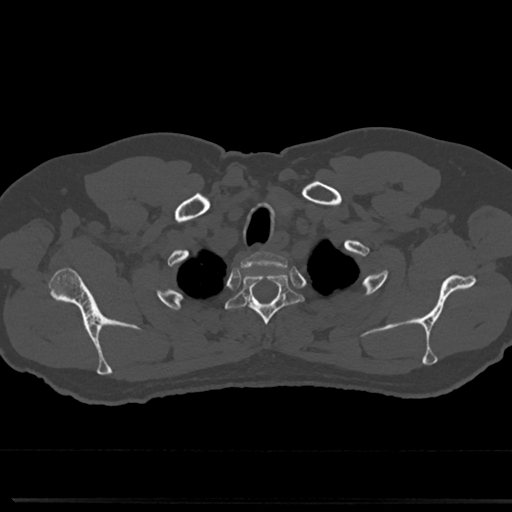
CT including the spine, one axial slice; position 641 of 817 along the scan axis; bone window (W 1800 / L 400 HU); 512 × 512 image matrix, field of view 355 × 355 mm. Male patient, age 61 years. Case-level facts recorded for this patient, not image findings: primary cancer: prostate.
Outlined on this slice (semi-automatically segmented with operator editing):
- T1 vertebra: bounding box (x1, y1, x2, y2) in pixels: (254, 253, 260, 257)
- T2 vertebra: (230, 266, 297, 352)